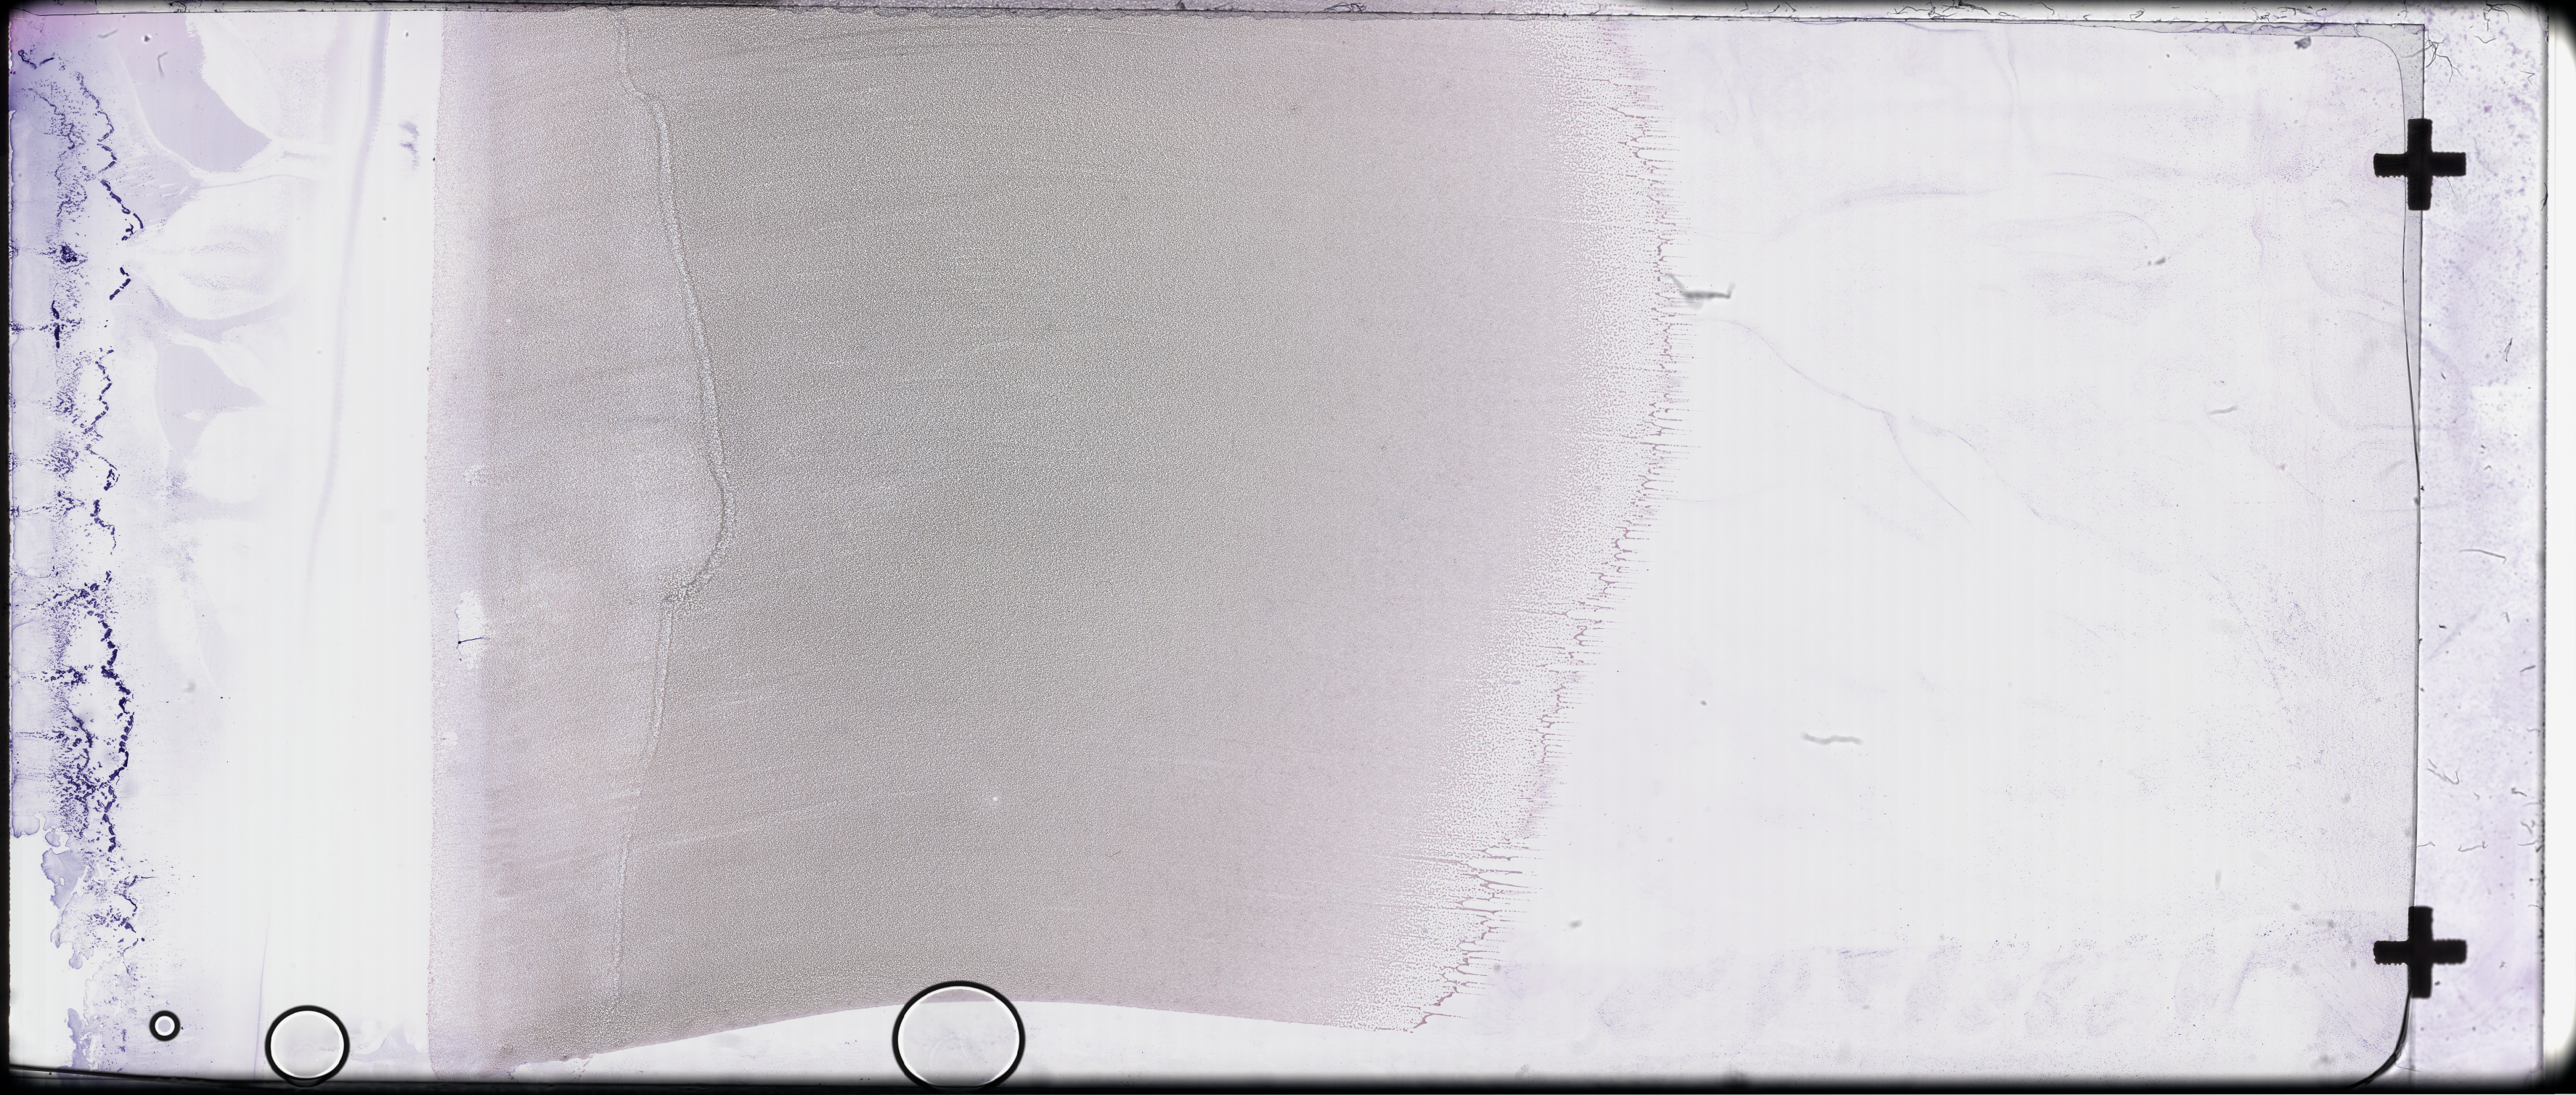
Whole-slide image of a whole blood smear, Wright-Giemsa stain — whole scanned area (about 57.3 x 24.4 mm) shown as a low-resolution overview, specimen time point: collected on treatment. Patient sex: female.
* from a patient with: Plasma Cell Myeloma